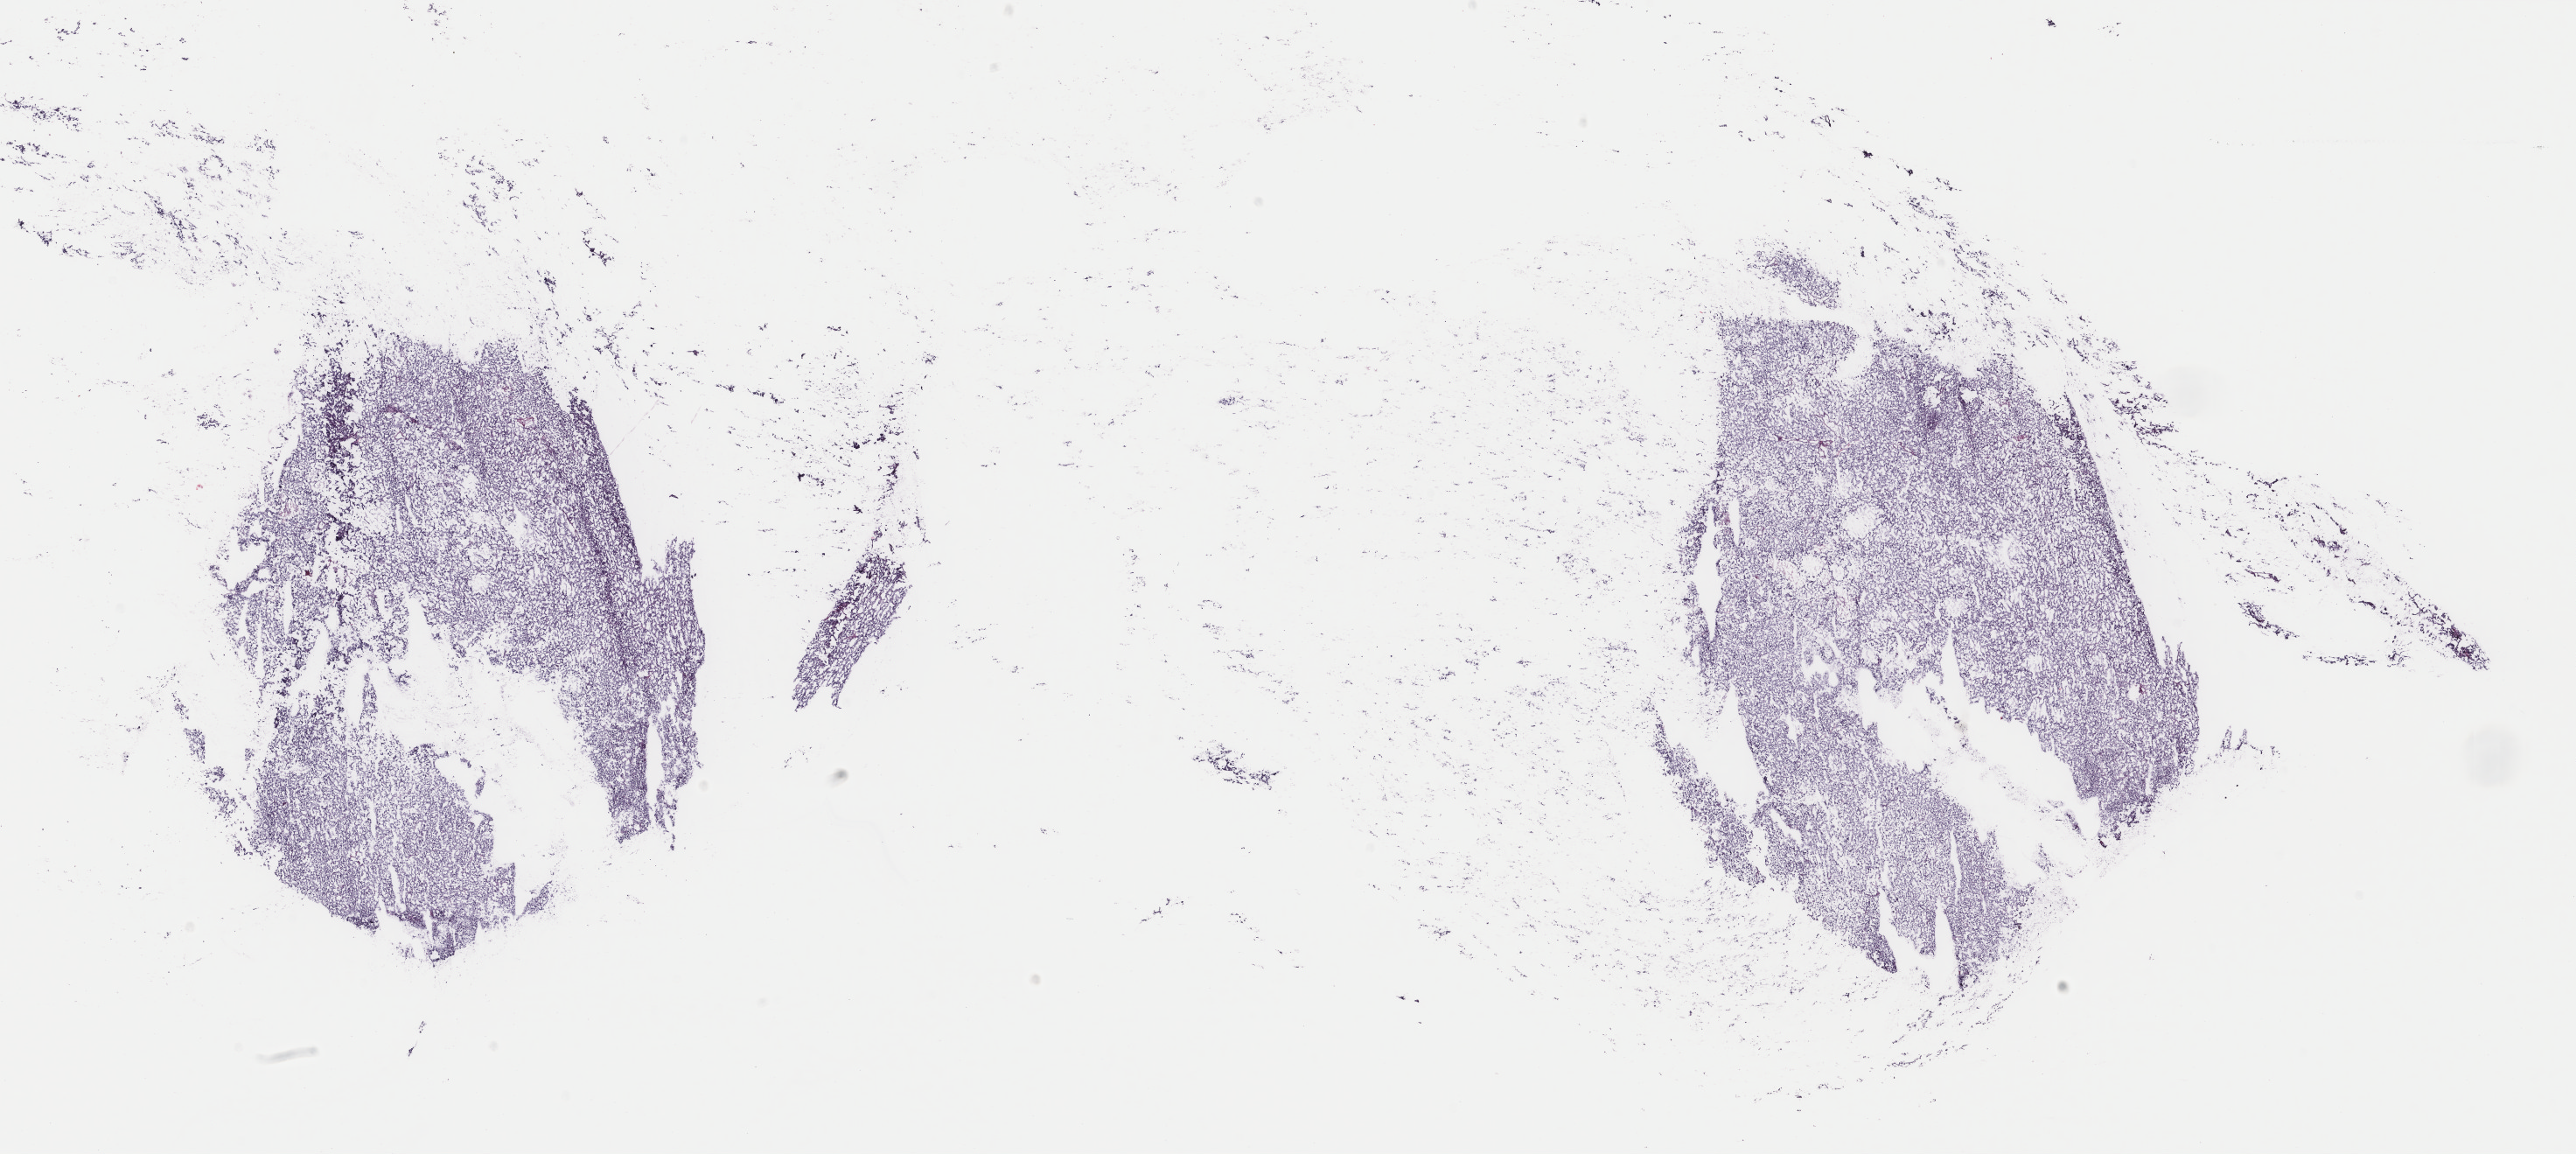
Whole-slide histology image, H&E, whole scanned area (about 23.4 x 10.5 mm) shown as a low-resolution overview. Frozen section from the top of the tissue portion. Adrenal gland, primary tumour sample. Female, age 37 years at initial diagnosis. Pathologist review of this section (percent, as recorded): tumour cells 90%, tumour nuclei 95%, normal cells 0%, stromal cells 10%, necrosis 0%. Infiltration values recorded for this section: lymphocyte infiltration 0%, monocyte infiltration 0%, neutrophil infiltration 0%.
Histologic diagnosis: Pheochromocytoma, NOS.